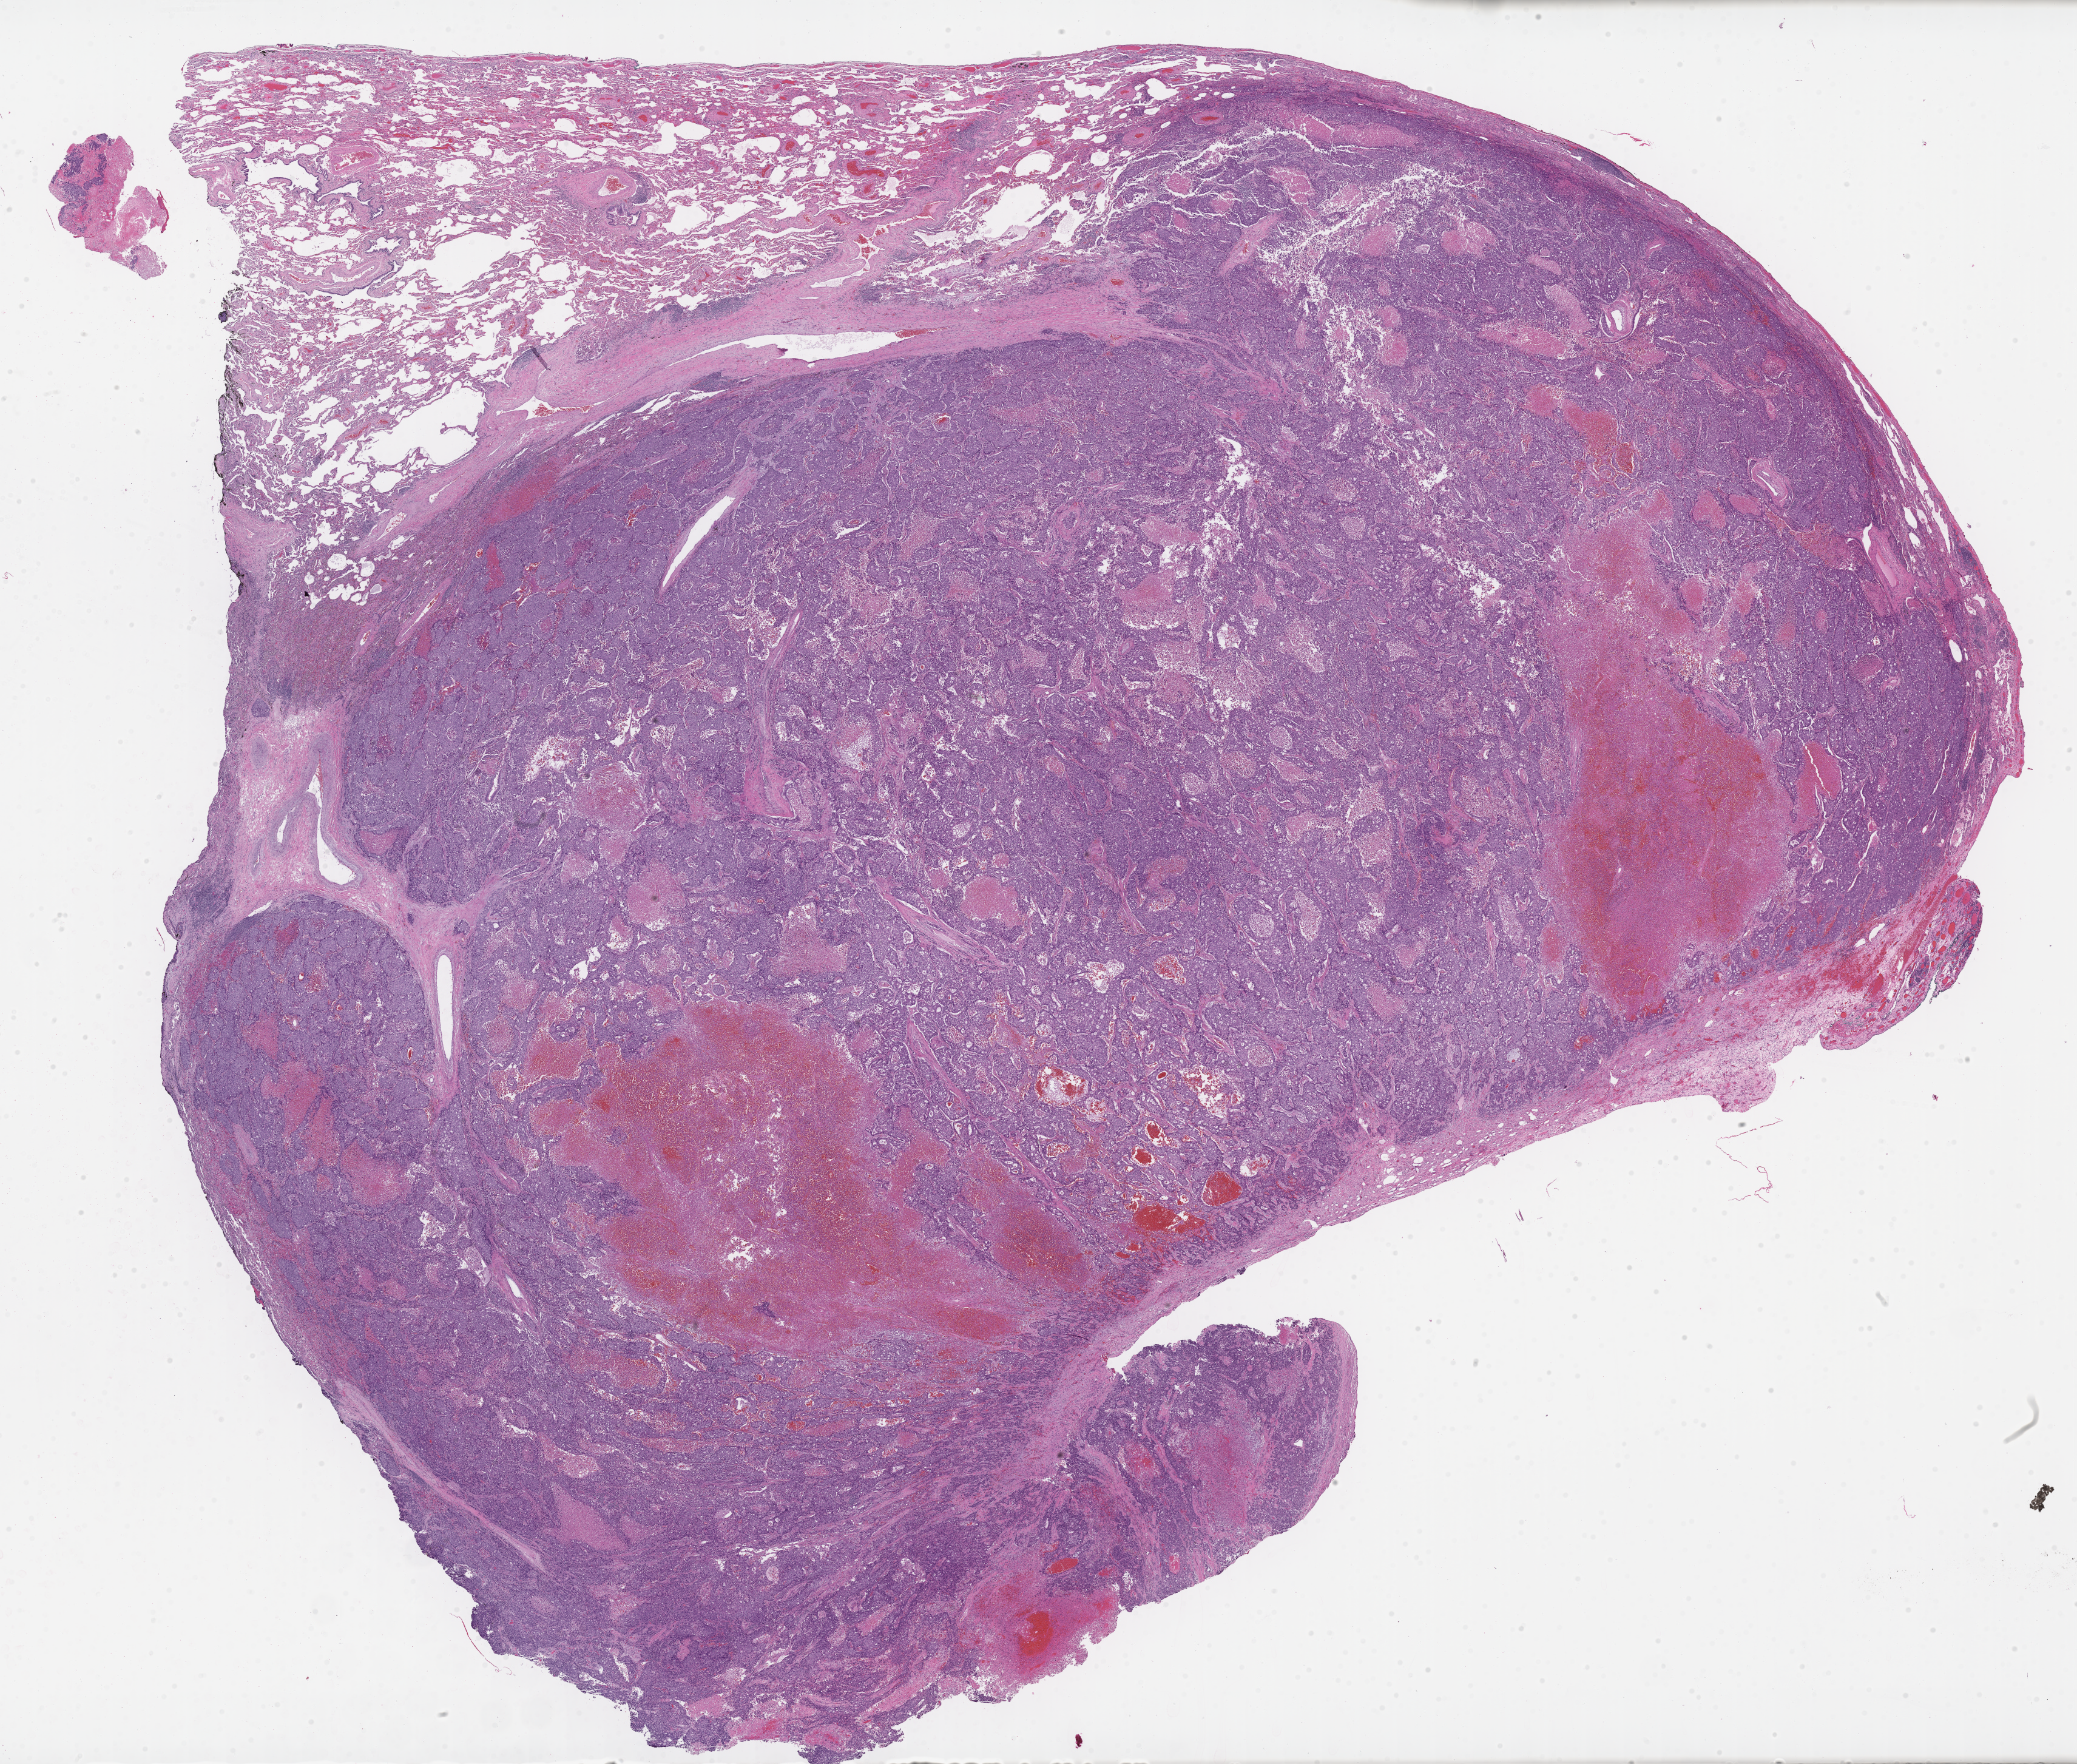
Whole-slide image, hematoxylin and eosin (H&E) stain, a low-resolution overview of the entire scanned area, about 27.6 x 23.5 mm. Formalin-fixed paraffin-embedded section. Specimen: primary tumor. Anatomic site: upper lobe of left lung. Patient: male, age at initial diagnosis 60 years. Tumor grade: G3 (poorly differentiated). Composition of this section per pathologist review: tumor cells 80%, tumor nuclei 90%, stromal cells 0%, necrosis 10%, normal cells 10%. Inflammatory infiltration, as recorded: lymphocyte infiltration 0%, monocyte infiltration 0%, neutrophil infiltration 0%.
• AJCC pathologic stage: Stage IIIA
• histologic diagnosis: Solid carcinoma, NOS
• section: top of the tissue portion